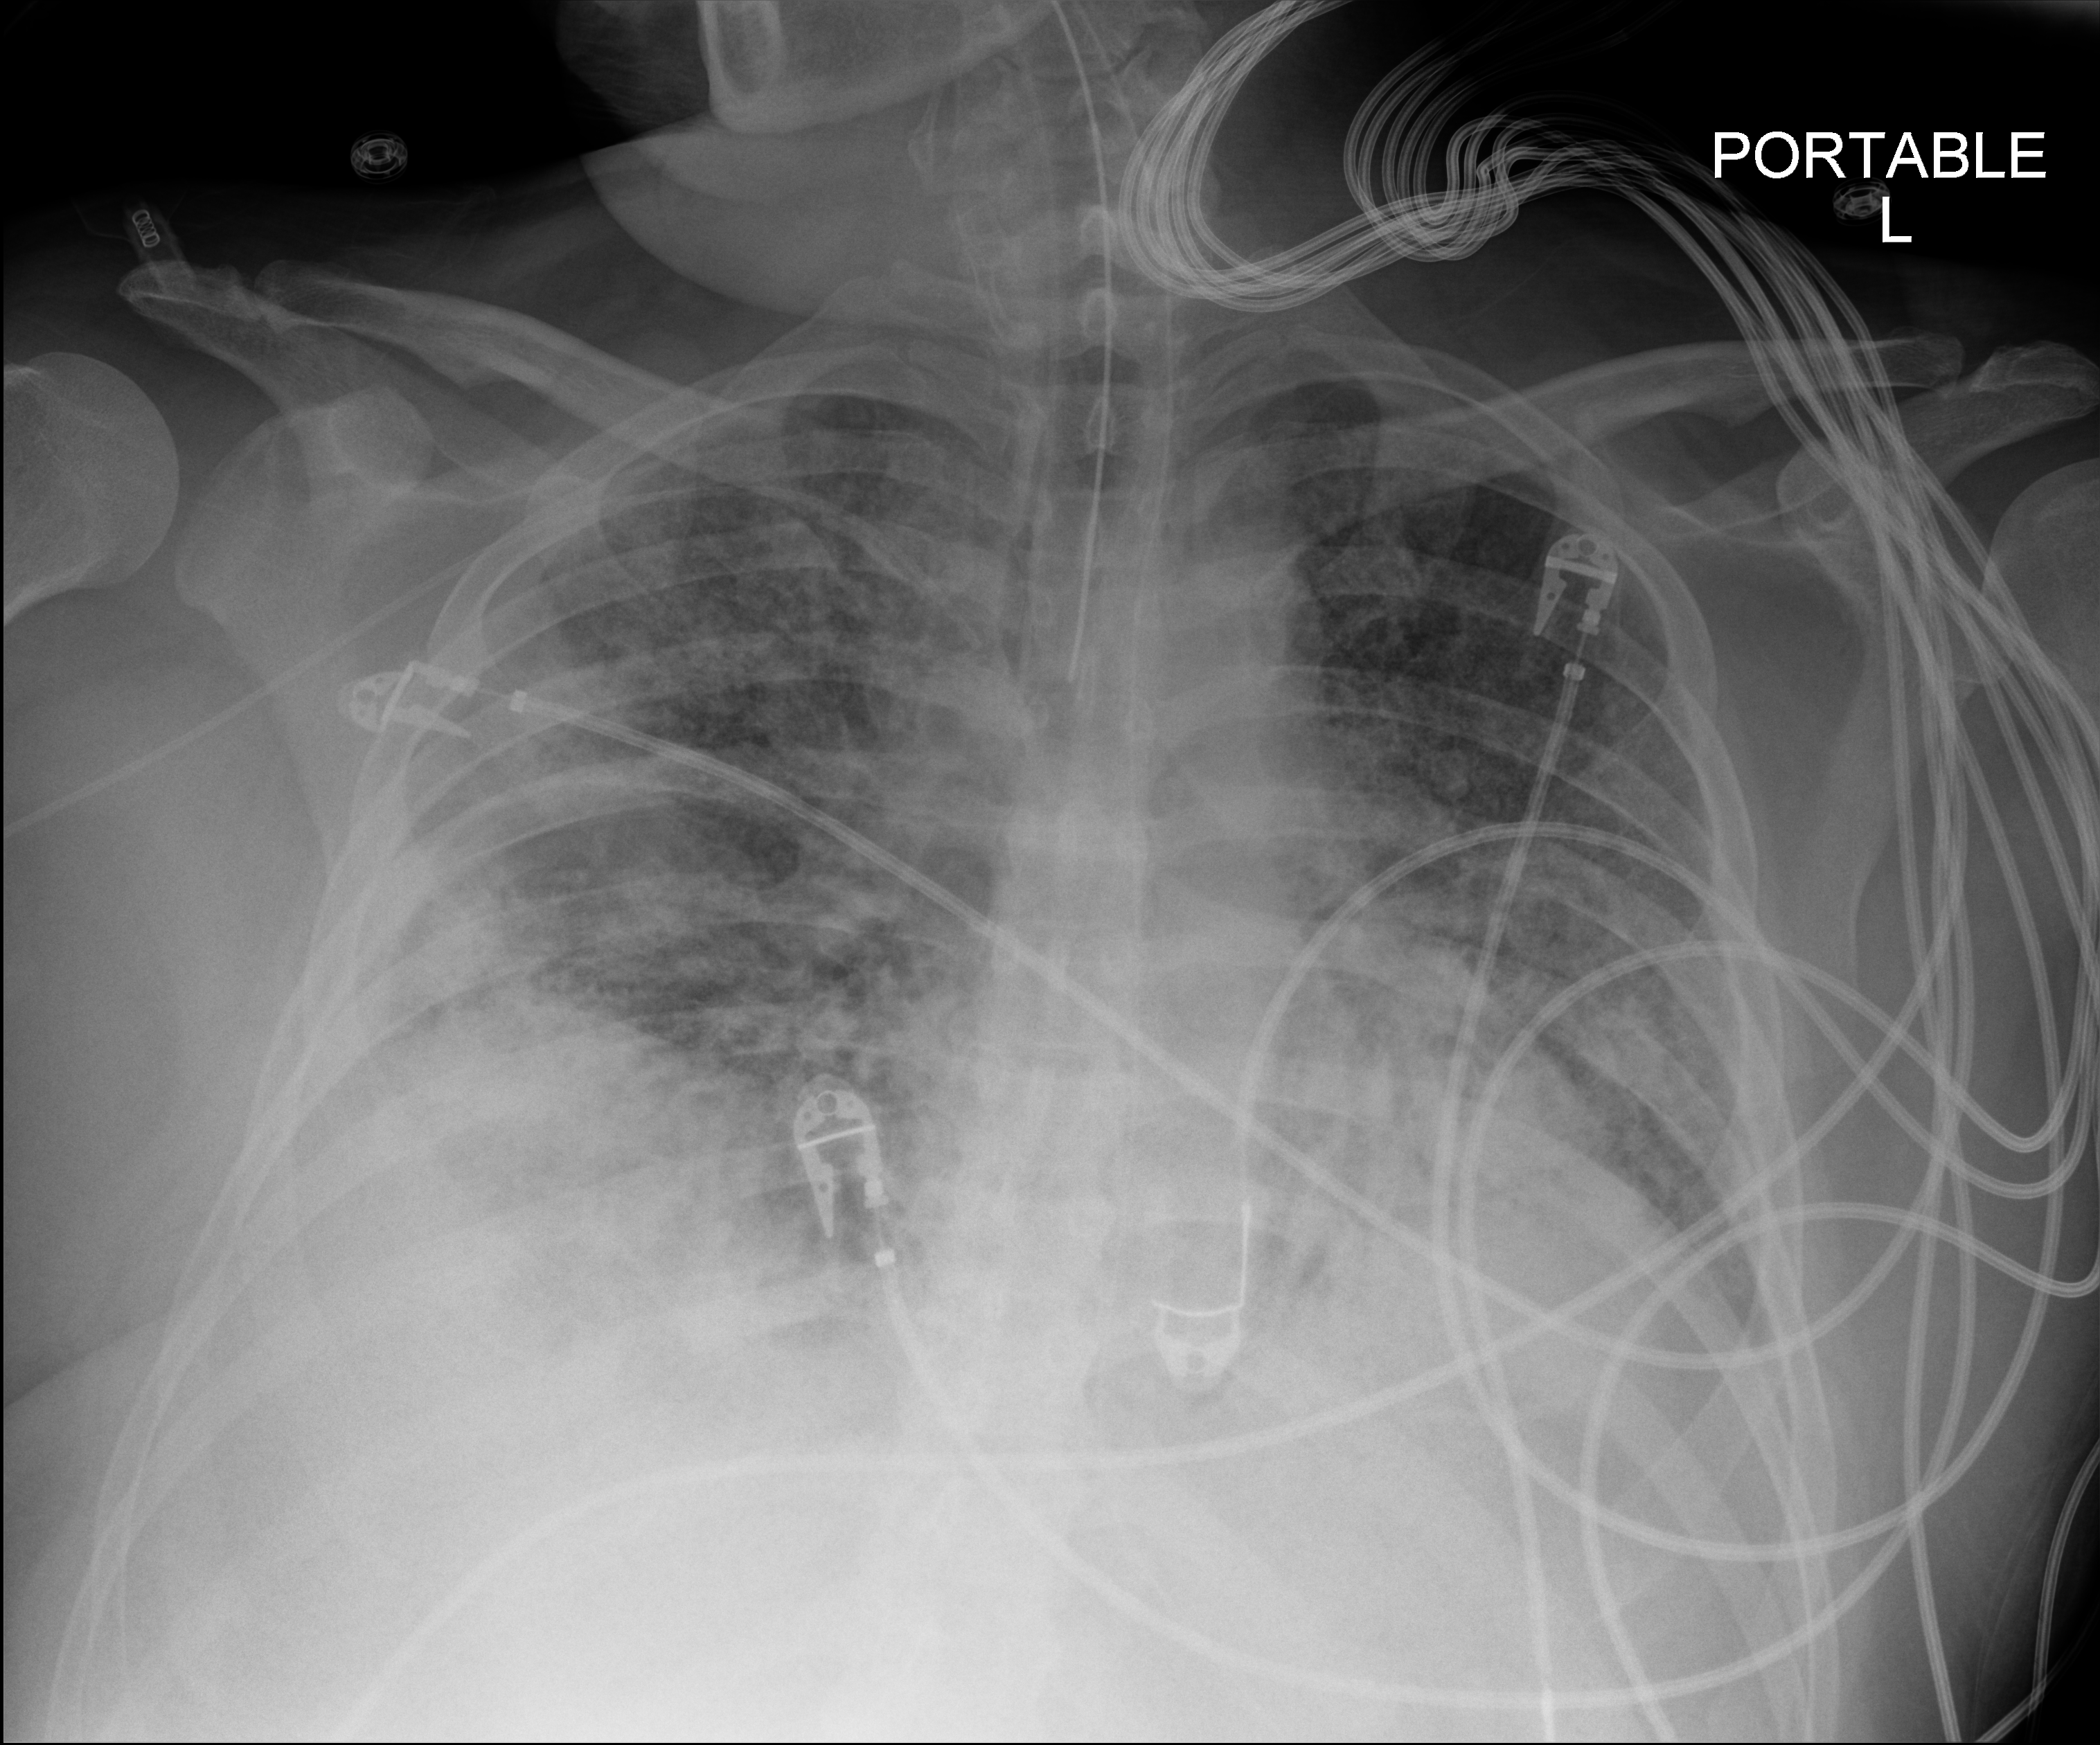
Portable chest radiograph. Male patient hospitalised with COVID-19, age 18–59 years.
From the hospital-stay record, not from the radiograph (when in the stay this image was taken is not recorded):
- mechanically ventilated during this hospital stay: yes
- diabetes (admission record): no